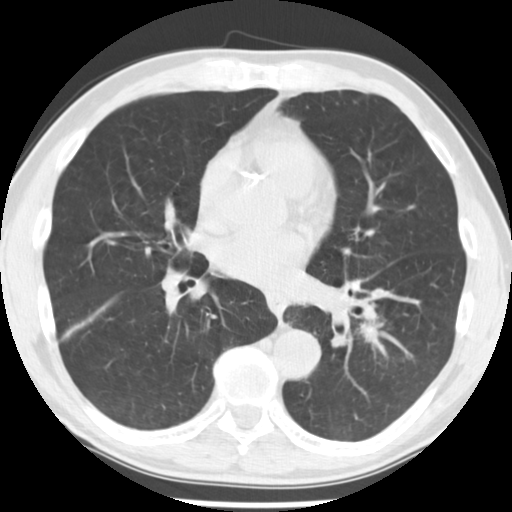
Axial slice from a low-dose chest CT screening exam, third annual screen, lung window (W 1500 / L -600 HU), 2.5 mm slice thickness, 120 kVp, slice 112 of 242 in the series. Male, age 64 years at enrolment. Current smoker at enrolment.
Expert-annotated lung lesion, bounding box [x1, y1, x2, y2] px = [352, 318, 390, 348]. No non-calcified nodule or mass ≥4 mm was recorded by the screening reader at this exam. Later outcome: lung cancer diagnosed 203 days after this screen — adenocarcinoma, NOS, left lower lobe, stage IV (AJCC 6th edition), 44 mm at pathology.